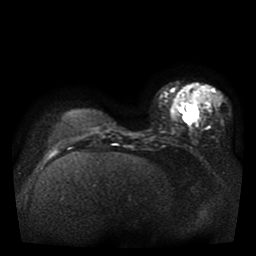
Breast MRI, one axial slice. Slice 12 of 41 in the series (ordered by position). Diffusion-weighted series; image 2 of 4 stored at this slice position (different b-values; order by instance number). 1.5 T. 5 mm slice thickness. 256 × 256 image matrix, field of view 330 × 330 mm. Female patient.
Annotated regions visible in this slice (outlined manually by an expert reader):
- tumour on diffusion-weighted imaging: bounding box <183,106,197,122> (left, top, right, bottom; pixels)